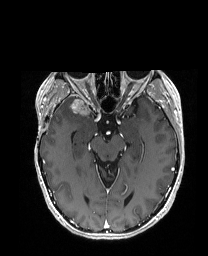
Brain MRI from a brain-tumour surgery series, one axial slice; position 109 of 192 along the scan axis; T1-weighted post-contrast; 1 mm slice thickness; 208 × 256 image matrix, field of view 203 × 250 mm. Case-level facts recorded for this patient, not image findings: histopathology: Metastatic Carcinoma from Breast primary; tumour location: Right Frontal.
Outlined on this slice (outlined manually by an expert reader):
- tumour: bounding box (x1, y1, x2, y2) in pixels: (67, 97, 88, 114)